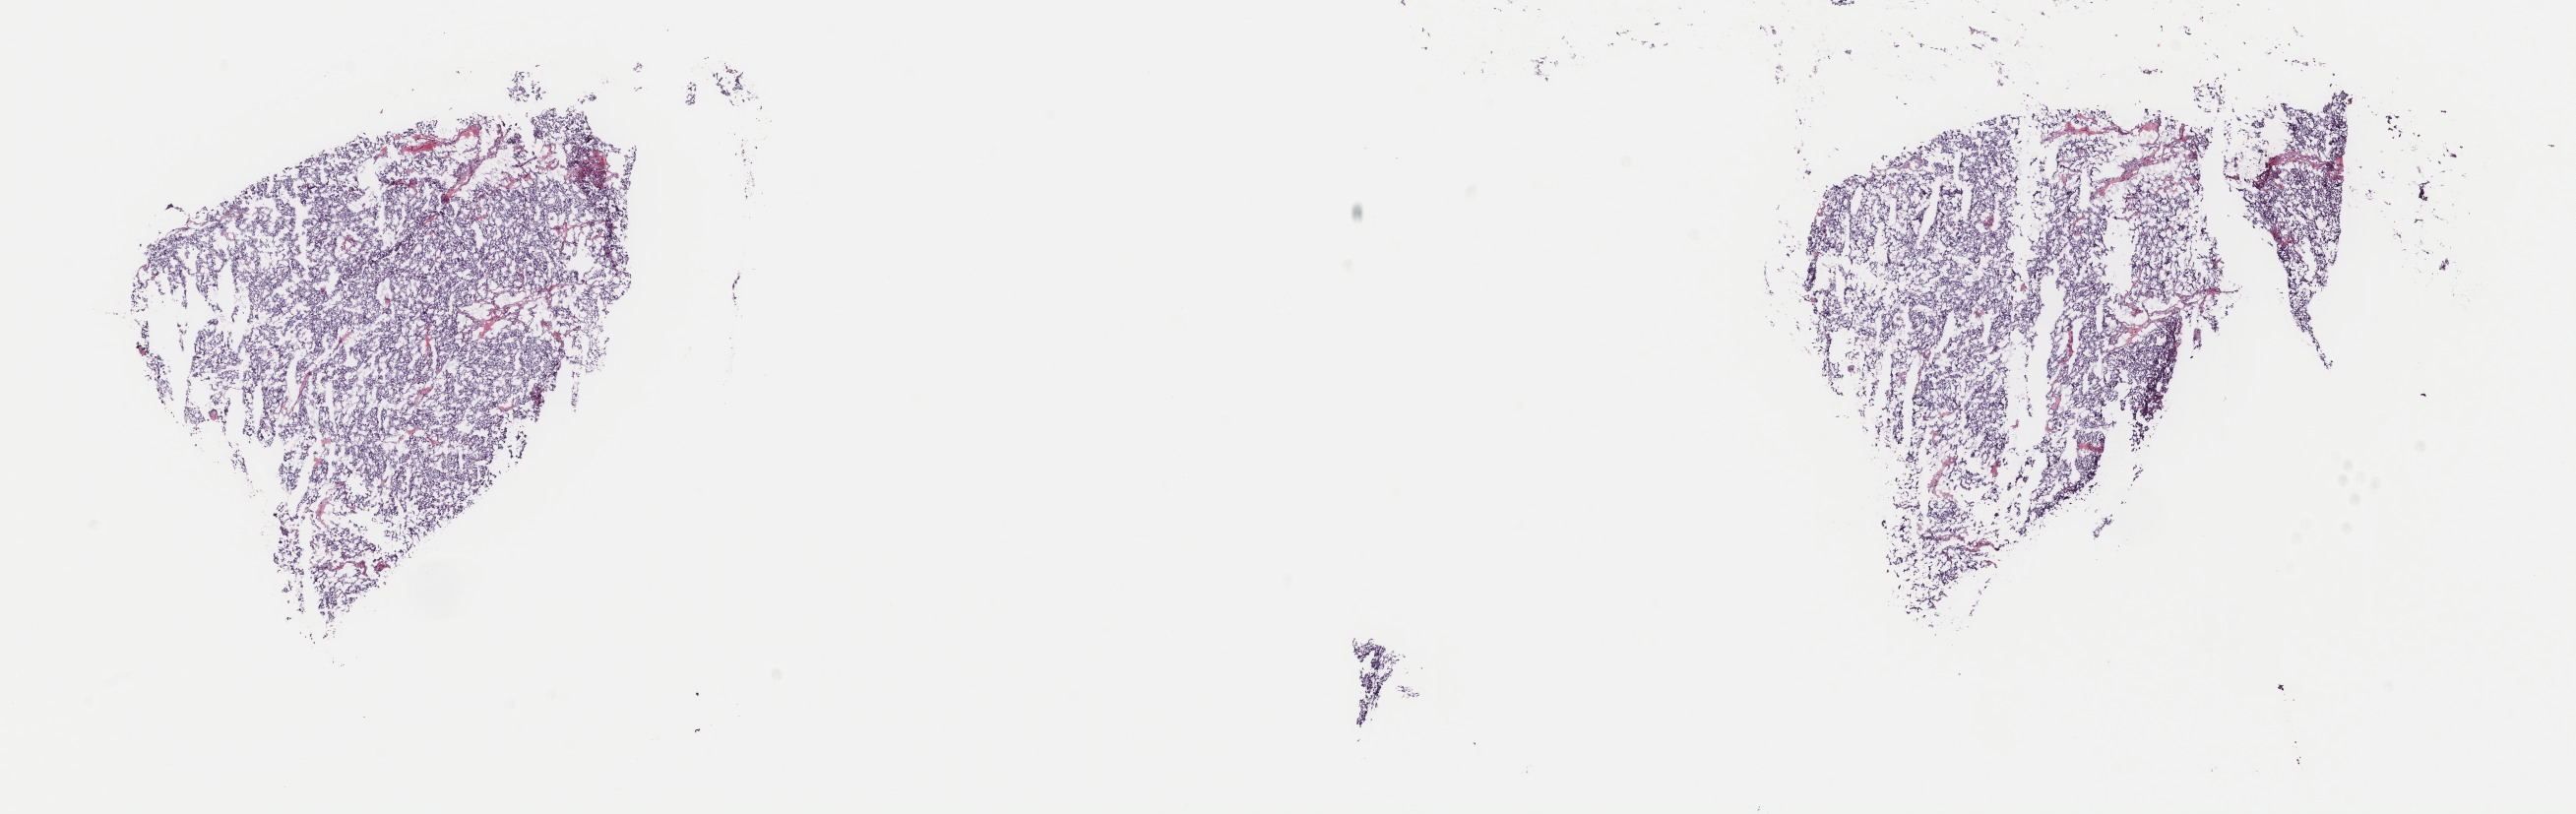
Whole-slide histology image, Hematoxylin and eosin (H&E) stained, whole scanned area (about 20.8 x 6.6 mm) shown as a low-resolution overview, frozen section from the top of the tissue portion, primary tumour sample from the adrenal gland. Male patient; age at initial diagnosis 55 years. Pathologist review of this section (percent, as recorded): tumour cells 100%, tumour nuclei 95%, normal cells 0%, stromal cells 0%, necrosis 0%. Inflammatory infiltration, as recorded: lymphocyte infiltration 0%, monocyte infiltration 0%, neutrophil infiltration 0%.
Laterality: left. Pathologic diagnosis: Pheochromocytoma, NOS.